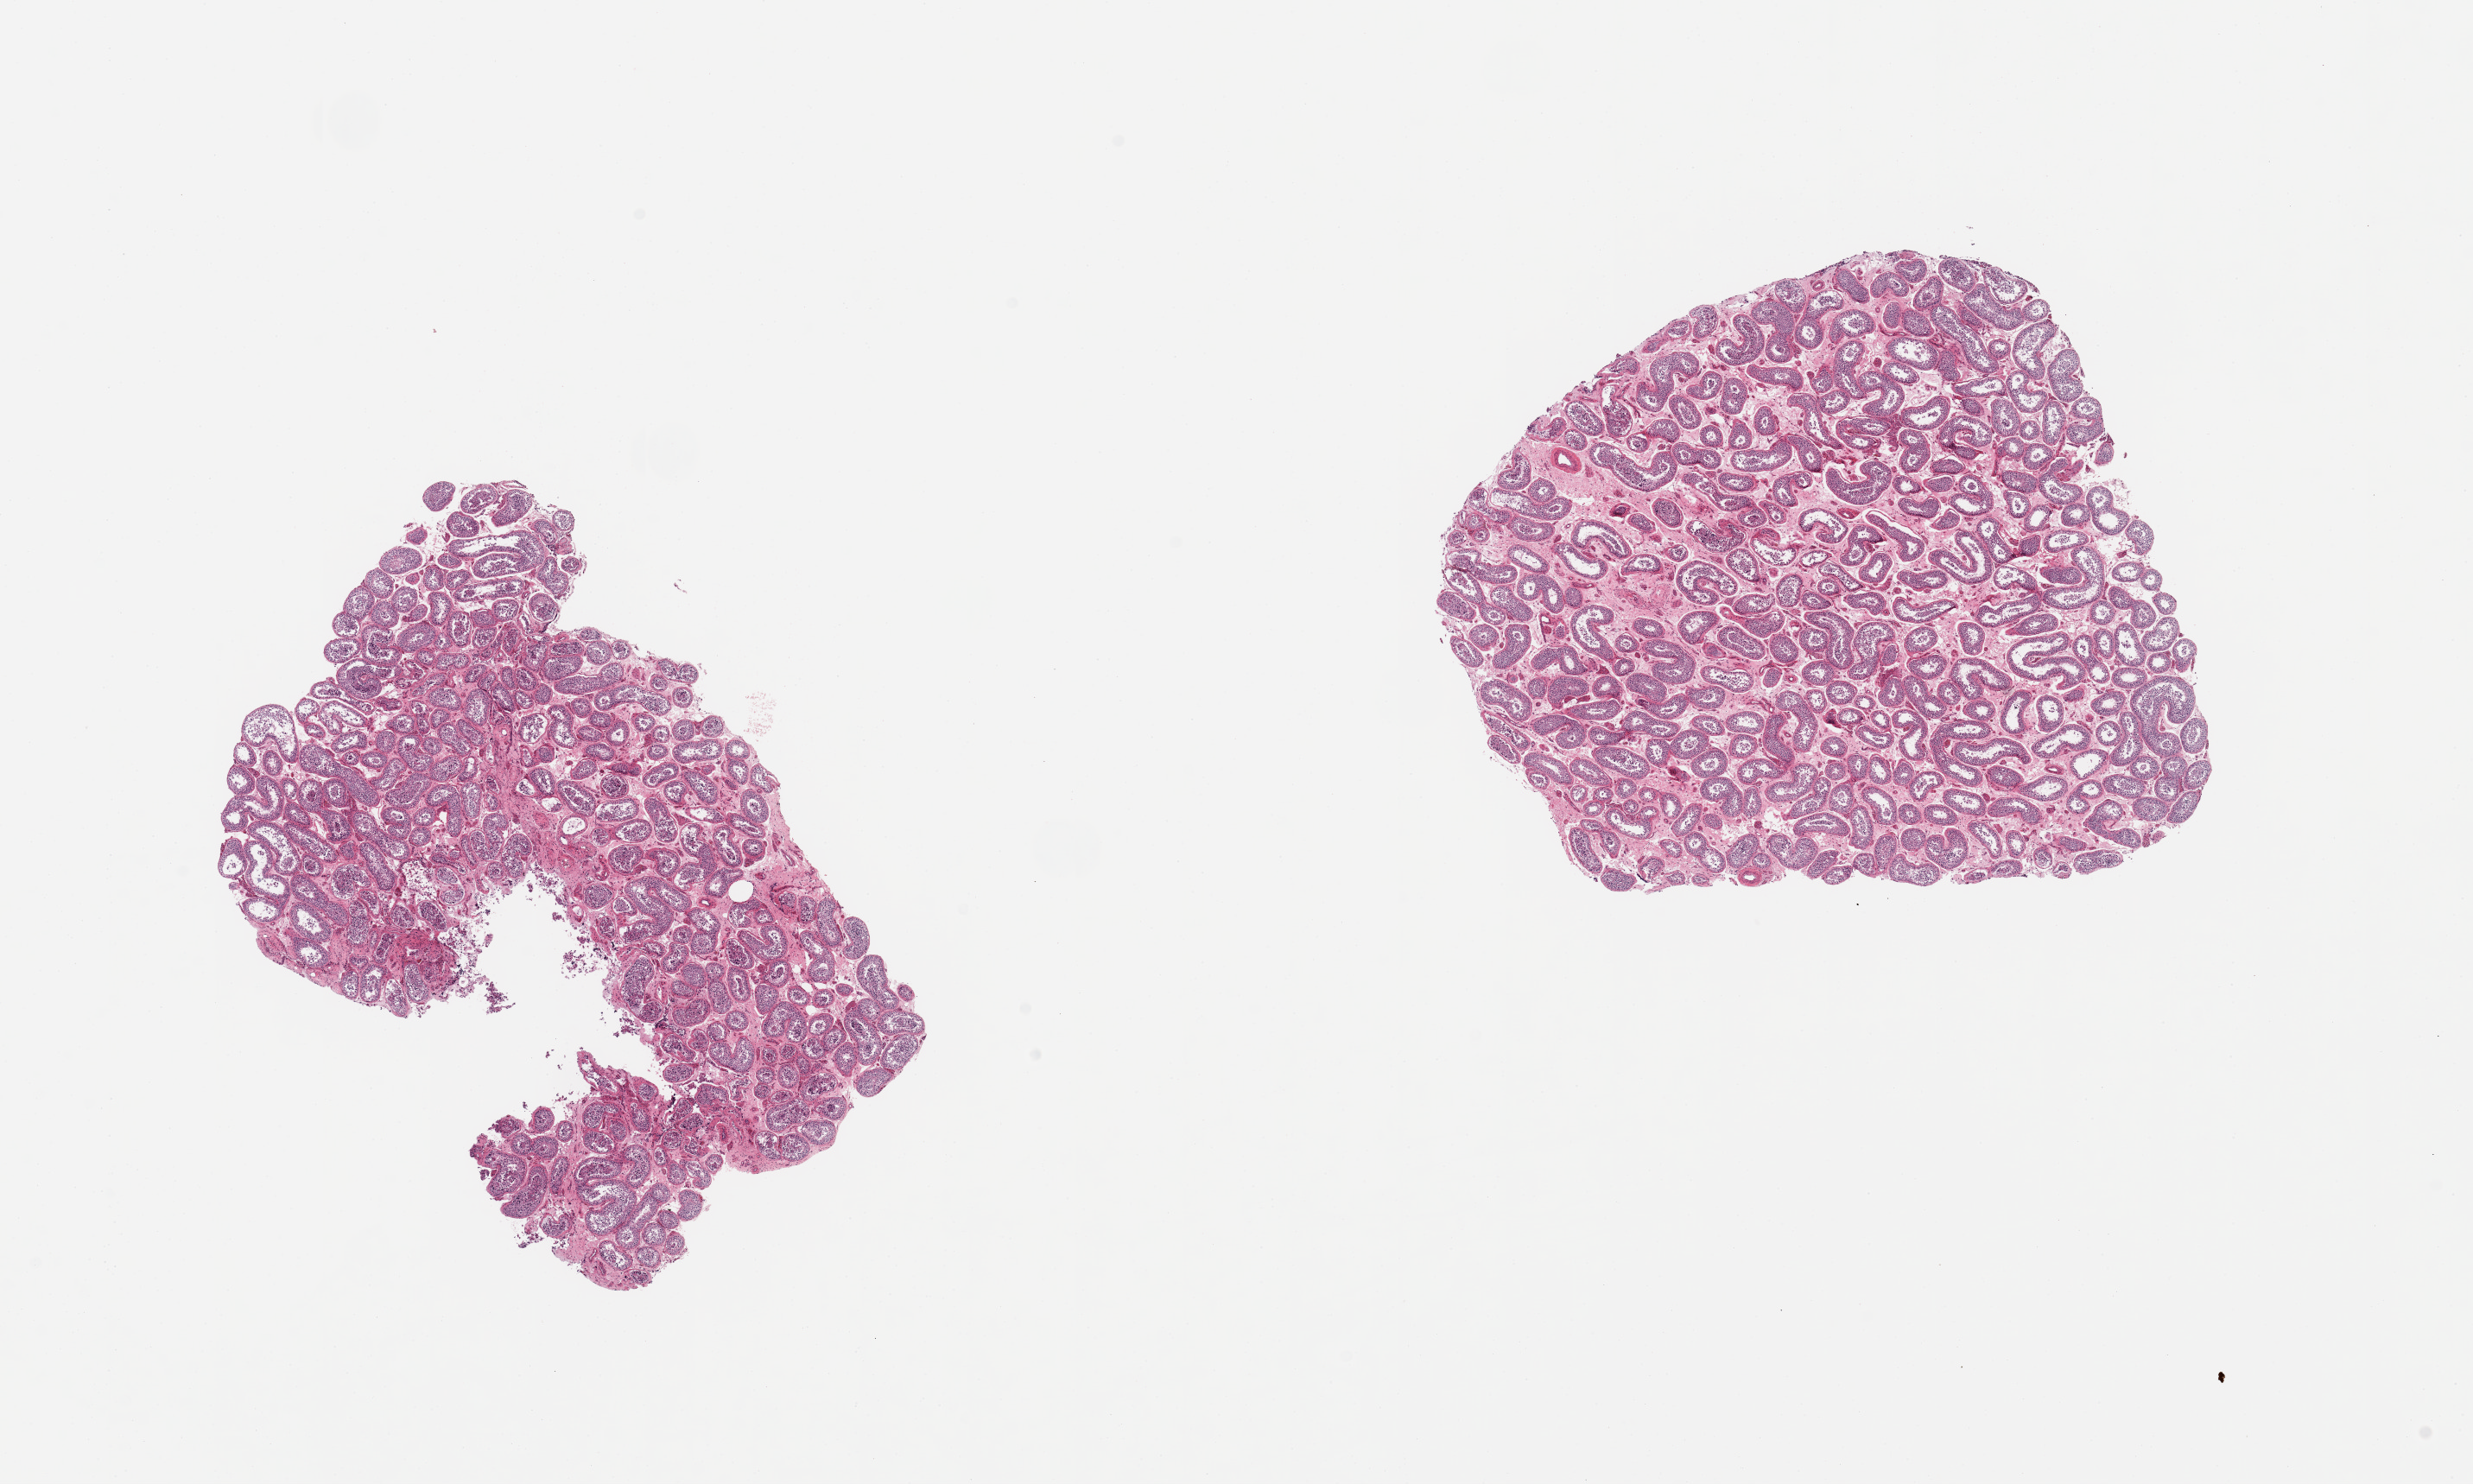
Digitized hematoxylin and eosin (H&E)-stained section, whole scanned area (about 22.6 x 13.6 mm) shown as a low-resolution overview. PAXgene-fixed paraffin-embedded (PFPE) section. Section of testis (target tissue). Donor tissue sample. Donor: male.
• reviewer comment on this tissue sample: 2 pieces, spermatogenesis present